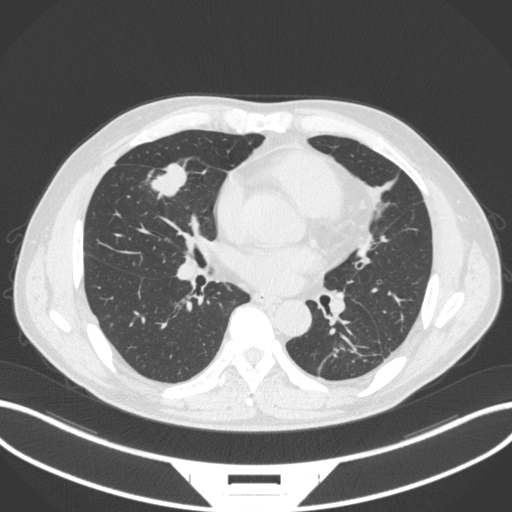
Chest CT, one axial slice; position 144 of 399 along the scan axis; reconstruction kernel B31f; lung window (W 1500 / L -600 HU); 1 mm slice thickness; 512 × 512 image matrix, field of view 400 × 400 mm. Male patient, age 59 years. Case-level facts recorded for this patient, not image findings: clinical TNM (as recorded): T2a N1 M0.
Structures marked on this image (rectangle marked by the reading radiologist):
- lung tumour (recorded histology: adenocarcinoma): bounding box [x1, y1, x2, y2] px = [148, 164, 190, 203]